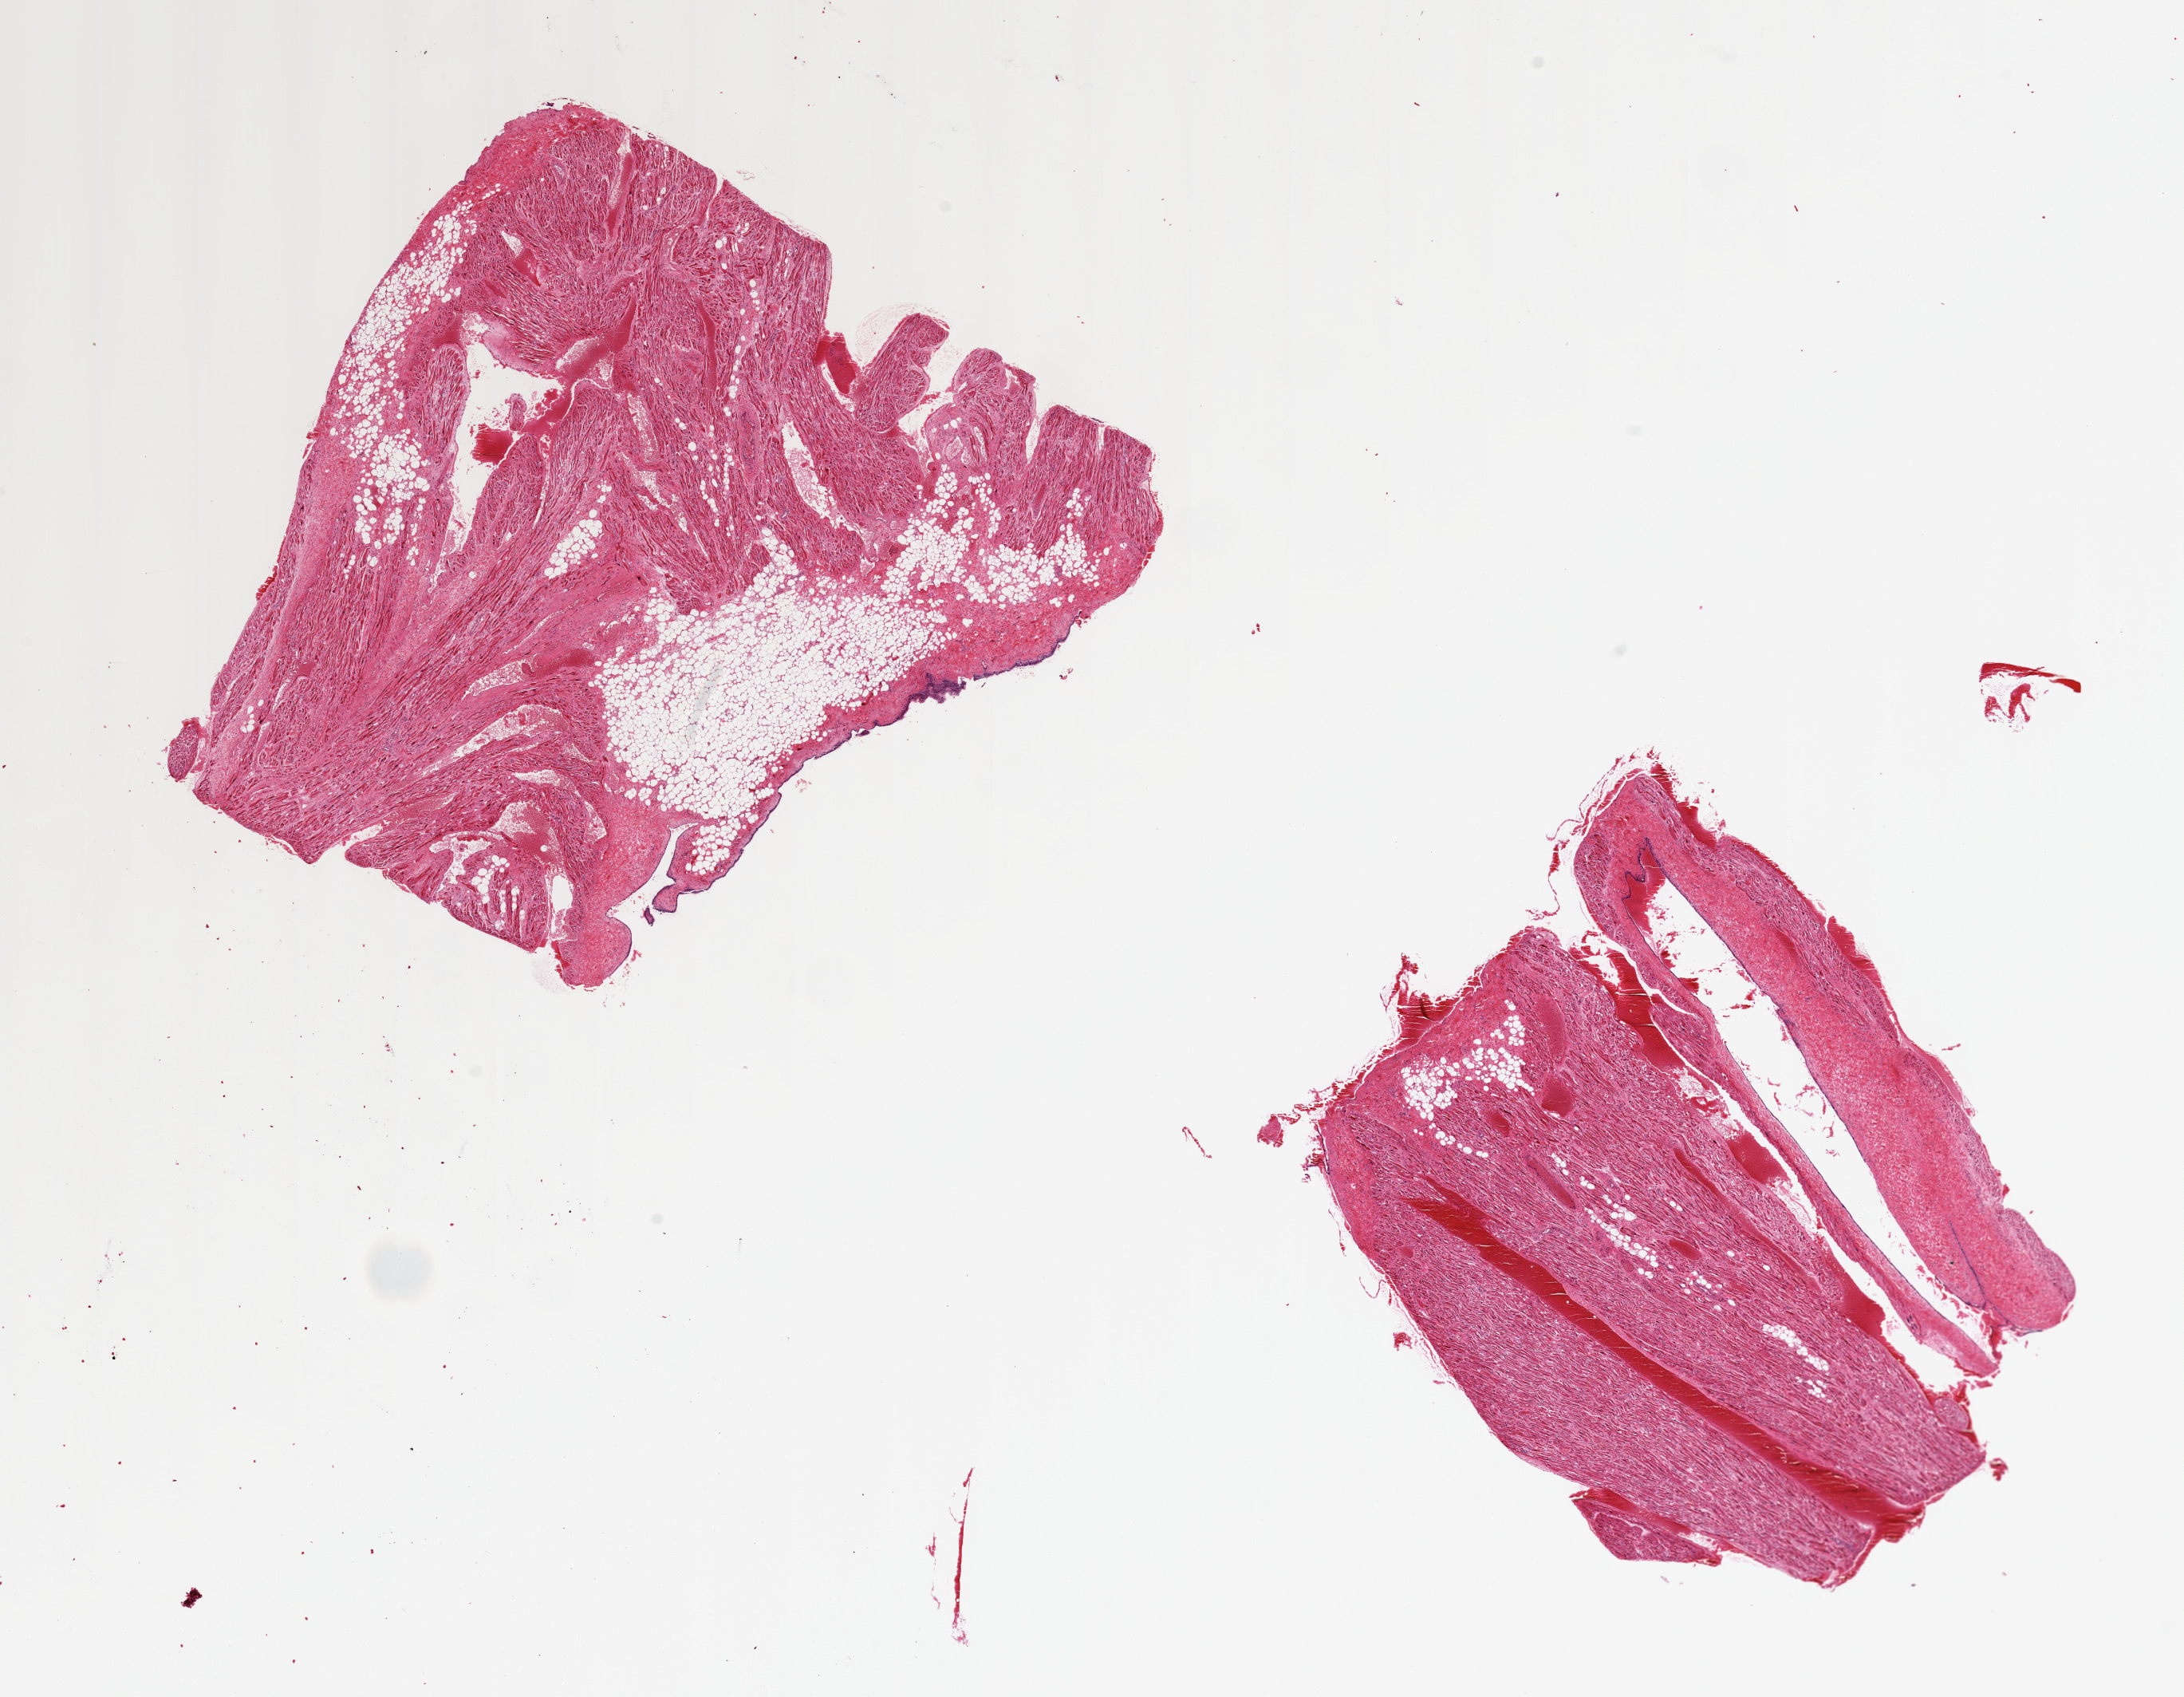
Digitized H&E-stained section, brightfield, low-resolution overview of the scanned area, about 21.7 x 16.8 mm. PAXgene-fixed, paraffin-embedded tissue. Target tissue: auricular appendage. Donor tissue sample. Donor sex: male.
* review note (as recorded): 2 pieces, 8x8 & 8x6mm; Moderate interstitial fibrosis. 40 and 1, 0% internal adipose